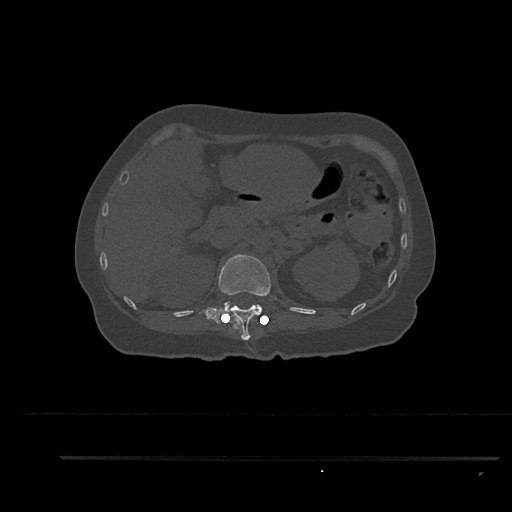
CT including the spine, one axial slice; position 248 of 797 along the scan axis; reconstruction kernel Br40s/3; bone window (W 1800 / L 400 HU); 512 × 512 image matrix. Female patient, age 44 years. From the clinical record (not read from this slice): primary cancer: renal.
Annotated regions visible in this slice (semi-automatically segmented with operator editing):
- T12 vertebra: bounding box [x1, y1, x2, y2] px = [198, 254, 271, 340]